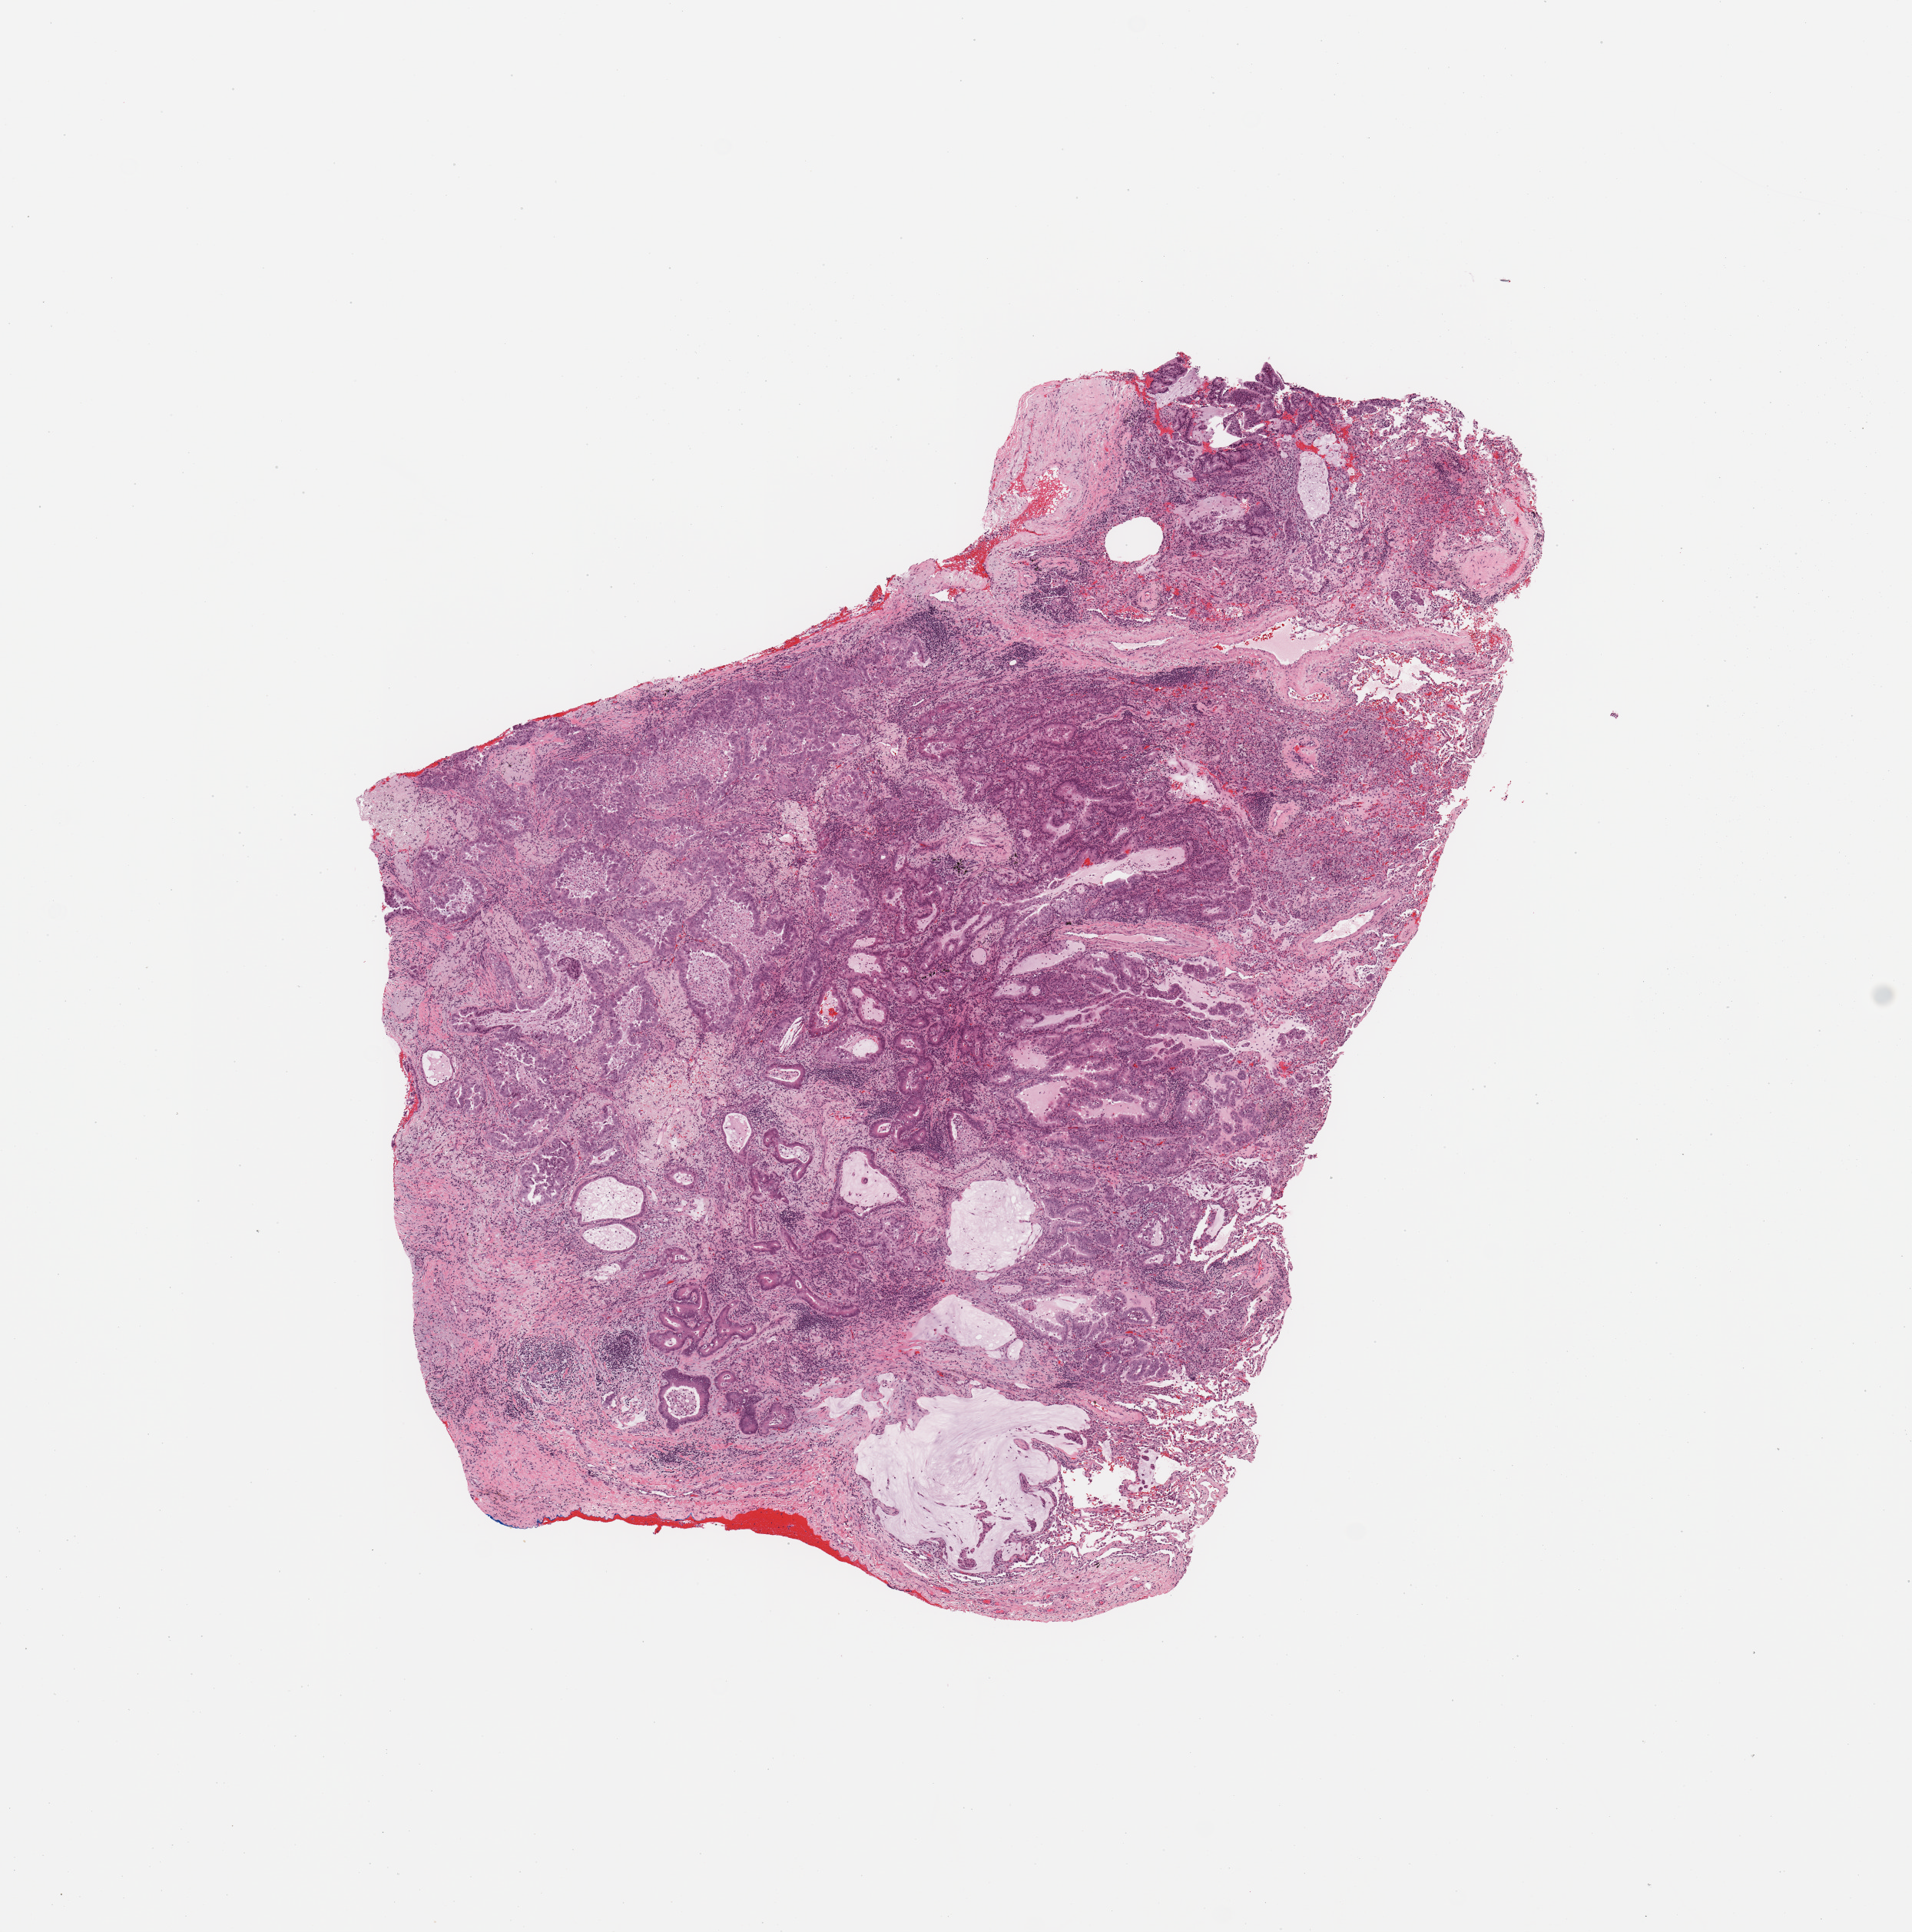
Whole-slide histology image, H&E-stained — whole scanned area (about 9.8 x 9.9 mm, slide scanned at 20x) shown as a low-resolution overview; tumour tissue sample, lung. Male, 81 y/o. Histologic grade: G2 (moderately differentiated).
Histologic diagnosis: Adenocarcinoma, NOS. AJCC pathologic stage: IIIA. Primary tumour site (as recorded): left lower lobe.